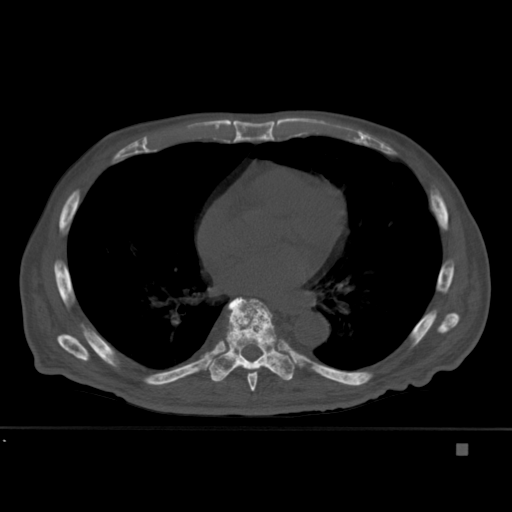
CT including the spine, one axial slice. Position 268 of 451 along the scan axis. Bone window (W 1800 / L 400 HU). 1.5 mm slice thickness. 512 × 512 image matrix. Patient: male, 75 years. Case-level facts recorded for this patient, not image findings: primary cancer: prostate.
Outlined on this slice (semi-automatically segmented with operator editing):
- T7 vertebra: bounding box (x1, y1, x2, y2) in pixels: (247, 304, 276, 391)
- T8 vertebra: (209, 297, 295, 382)